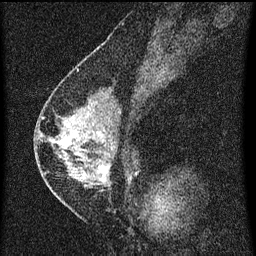
Breast MRI (dynamic contrast-enhanced), one sagittal slice; position 30 of 60 along the scan axis; dynamic contrast-enhanced series, image 2 of 3 at this slice position (ordered by acquisition); 1.5 T; TE 4.2 ms, TR 8 ms; 2 mm slice thickness; 256 × 256 image matrix, field of view 180 × 180 mm. Patient: female, 47 years.
Annotated regions visible in this slice (semi-automatically segmented with operator editing):
- analysis volume of interest (the breast-tissue region the enhancement analysis was run in; not a lesion): bounding box <42,92,134,199> (left, top, right, bottom; pixels)
- tumour enhancement mask (voxels above the 70 % enhancement threshold inside the analysis volume of interest): <42,132,109,177>